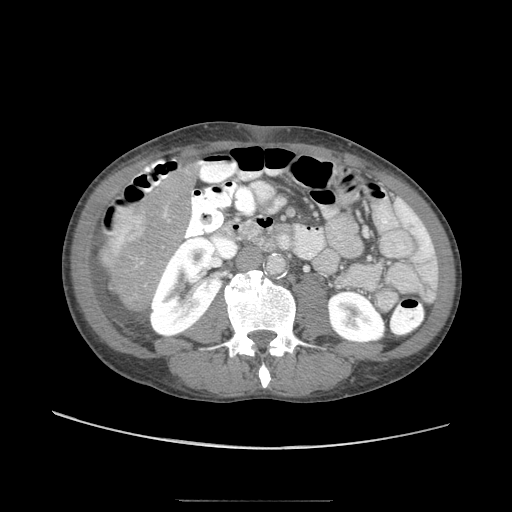
Contrast-enhanced abdominal CT (liver protocol), one axial slice; slice 12 of 103 in the series (ordered by position); 120 kVp; soft-tissue window (W 400 / L 40 HU); 2.5 mm slice thickness; 512 × 512 image matrix, field of view 380 × 380 mm. Case-level facts recorded for this patient, not image findings: diagnosis: hepatocellular carcinoma (patient treated with transarterial chemoembolisation; whether this scan precedes or follows treatment is not stated here); TNM stage (as recorded): Stage-IIIA; Child-Pugh class: A.
Annotated regions visible in this slice (semi-automatic segmentation, software-assisted and operator-edited):
- liver parenchyma outside the tumour (the mass and vessels are separate outlines, so this box may not span the whole liver): bounding box (x1, y1, x2, y2) in pixels: (96, 166, 196, 312)
- mass: (97, 197, 148, 268)